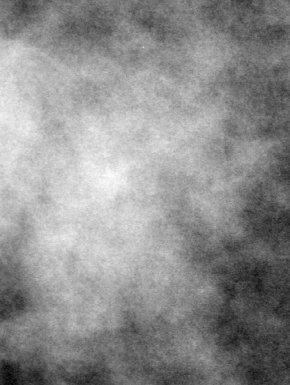
Cropped region of a digitized screen-film mammogram centred on a radiologist-marked abnormality, left breast, CC view.
Mass, shape lobulated, margins ill defined; BI-RADS assessment category 4; subtlety rating 1 on a 1 (subtle) to 5 (obvious) scale; pathology result (as recorded, not read from the image): malignant.